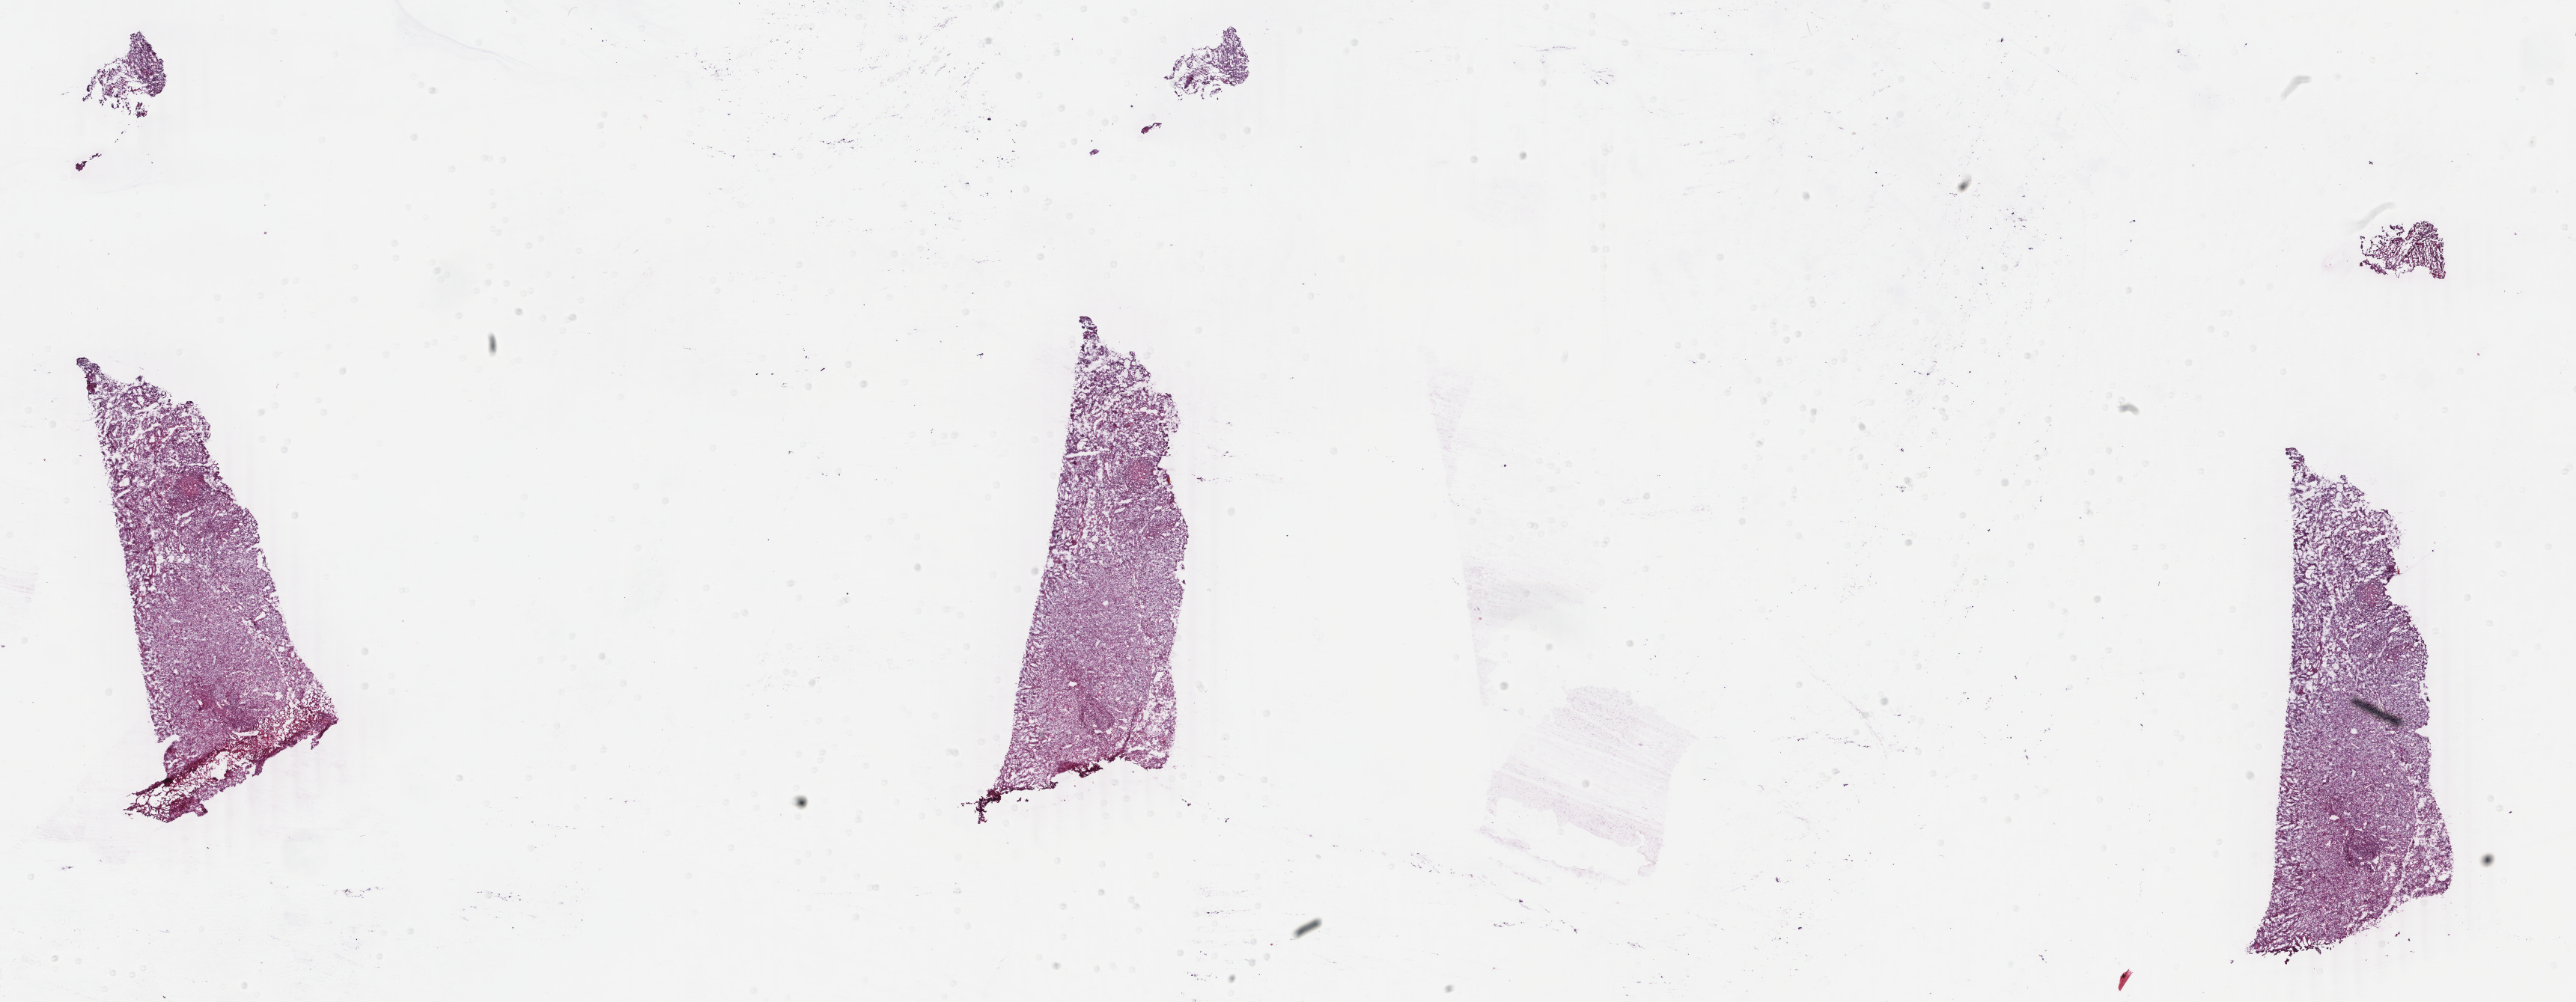
Digitized Hematoxylin and eosin (H&E) stained tissue section (whole slide) — low-resolution overview of the scanned area, about 27.4 x 10.6 mm (acquisition: 40x scan). Frozen section from the top of the tissue portion. Uterus, primary tumour sample. Female, age 81 years at initial diagnosis. Histologic grade: G3 (poorly differentiated). Pathologist review of this section (percent, as recorded): tumour cells 85%, tumour nuclei 80%, normal cells 14%, stromal cells 0%, necrosis 1%. Inflammatory infiltration, as recorded: lymphocyte infiltration 14%, monocyte infiltration 0%, neutrophil infiltration 0%.
FIGO stage: IIIC. Histologic diagnosis: Endometrioid adenocarcinoma, NOS (endometrium).